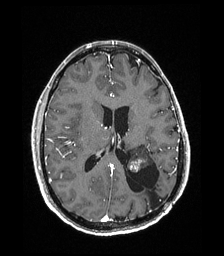
Brain MRI from a brain-tumour surgery series, one axial slice; T1-weighted post-contrast; 1 mm slice thickness; 224 × 256 image matrix, field of view 224 × 256 mm. From the clinical record (not read from this slice): histopathology: Low grade glioma; IDH mutation: no; tumour location: Left Parieto-Occipital Intraventricular.
Annotated regions visible in this slice (outlined manually by an expert reader):
- previous resection cavity: bounding box [x1, y1, x2, y2] px = [126, 163, 165, 208]
- tumour: [128, 144, 153, 172]